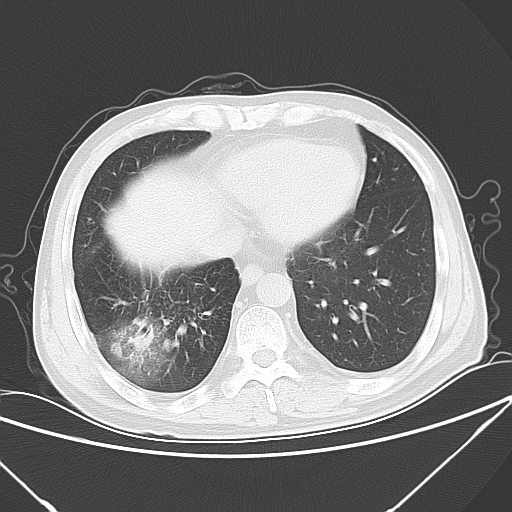
Chest CT, one axial slice. Lung window (W 1500 / L -600 HU). 5 mm slice thickness. 512 × 512 image matrix, field of view 364 × 364 mm. Patient: male, 54 years. Case-level facts recorded for this patient, not image findings: clinical TNM (as recorded): T2 N1 M0; histopathological grade: G3.
Structures marked on this image (rectangle marked by the reading radiologist):
- lung tumour (recorded histology: adenocarcinoma): bounding box <108,314,157,366> (left, top, right, bottom; pixels)